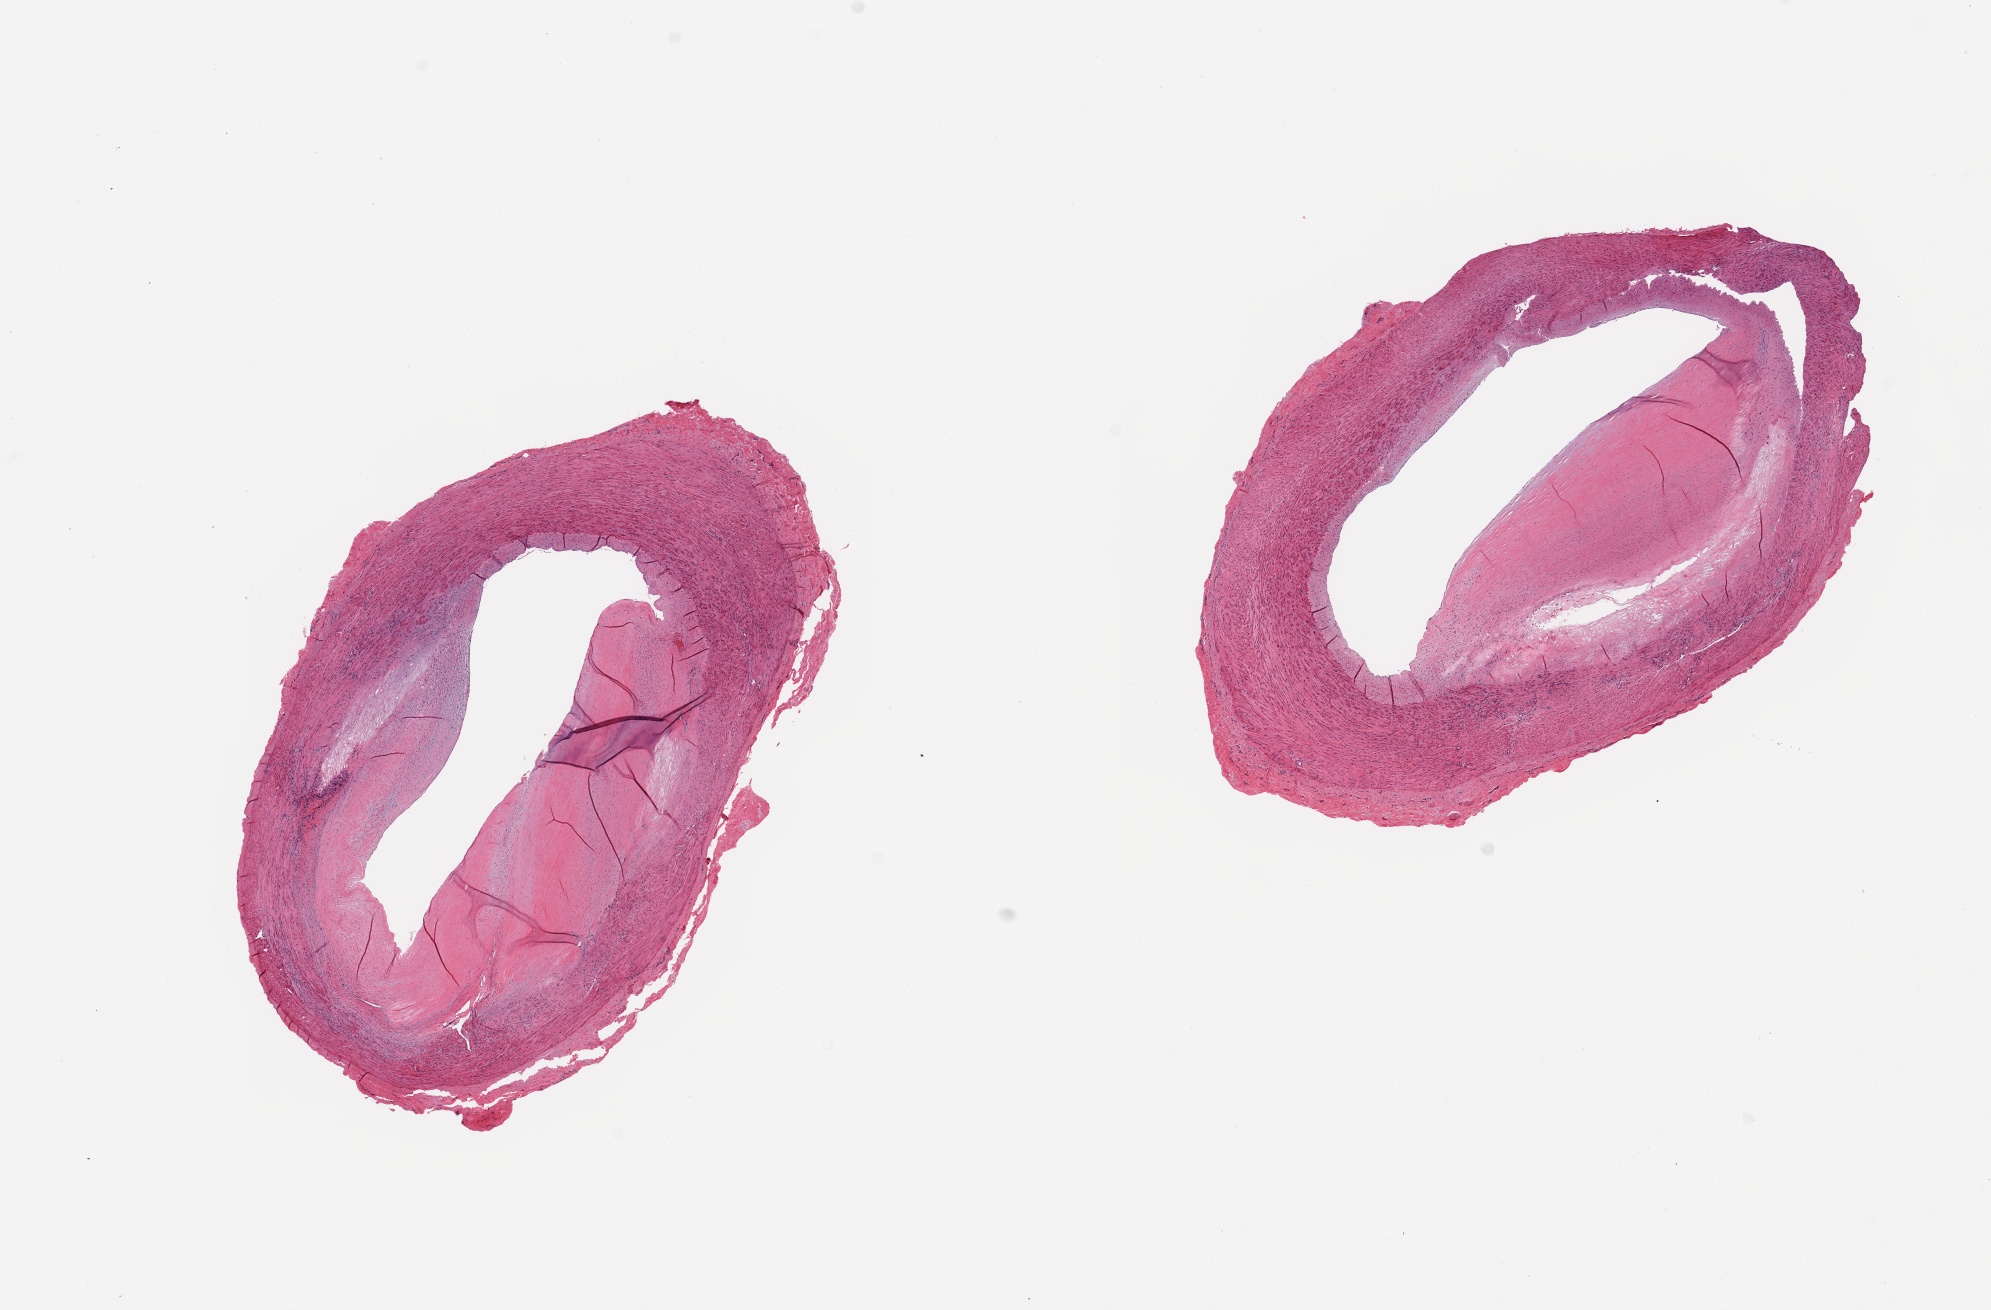
Whole-slide image, hematoxylin and eosin (H&E) stain, a low-resolution overview of the entire scanned area, about 15.8 x 10.4 mm (slide scanned at 20x), PAXgene-fixed paraffin-embedded (PFPE) section, sampled site (target tissue): tibial artery, tissue donor sample. Donor: male.
• review note (as recorded): 2 pieces; atherosclerotic plaquewith 75% luminal compromise